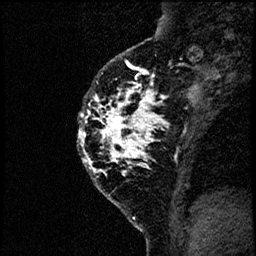
Breast MRI (dynamic contrast-enhanced), one sagittal slice. Slice 46 of 60 in the series (ordered by position). Dynamic contrast-enhanced study with each time point stored as its own series, time point 2 of 4 at this slice position (early post-contrast, ordered by acquisition time). 1.5 T. TE 4.2 ms, TR 17.6 ms. 256 × 256 image matrix, field of view 200 × 200 mm. Patient: female, 40 years. From the clinical record (not read from this slice): setting: breast cancer imaged before/during neoadjuvant chemotherapy; receptor status: HER2-positive.
Annotated regions visible in this slice (semi-automatically segmented with operator editing):
- analysis volume of interest (the breast-tissue region the enhancement analysis was run in; not a lesion): bounding box [x1, y1, x2, y2] px = [73, 55, 185, 206]
- tumour enhancement mask (voxels above the 100 % enhancement threshold inside the analysis volume of interest): [77, 60, 163, 164]